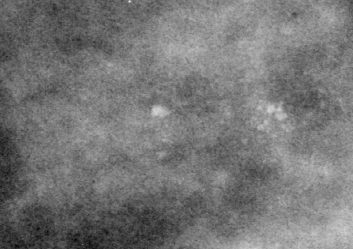
Cropped region of a digitized screen-film mammogram centred on a radiologist-marked abnormality, left breast, CC view, BI-RADS breast density category 2 (scale 1–4).
Calcifications, morphology pleomorphic, distribution clustered; BI-RADS assessment category 4; subtlety rating 3 on a 1 (subtle) to 5 (obvious) scale; pathology (as recorded): malignant.